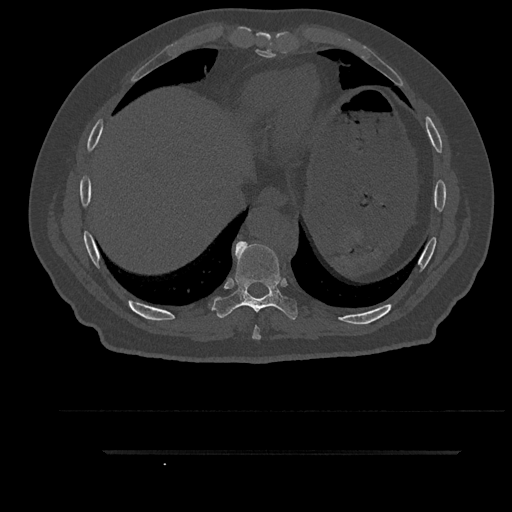
CT including the spine, one axial slice; slice 431 of 797 in the series (ordered by position); 120 kVp; bone window (W 1800 / L 400 HU); 0.5 mm slice thickness; 512 × 512 image matrix, field of view 432 × 432 mm. Patient: male, 63 years. From the clinical record (not read from this slice): primary cancer: renal; vertebrae with lytic lesions (as recorded): T8.
Structures marked on this image (semi-automatically segmented with operator editing):
- T8 vertebra: bounding box <252,325,261,340> (left, top, right, bottom; pixels)
- T9 vertebra: <212,241,298,320>